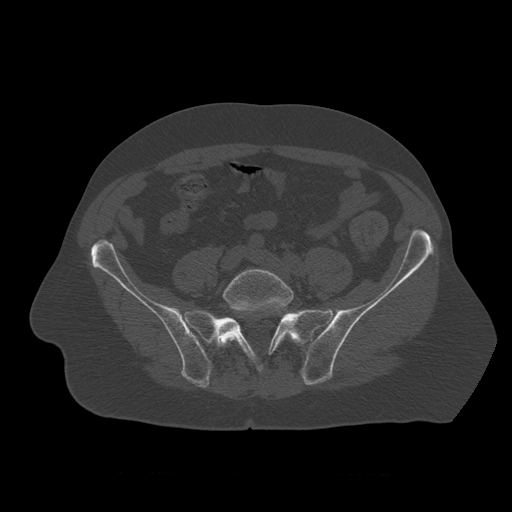
CT including the spine, one axial slice; position 244 of 450 along the scan axis; bone window (W 1800 / L 400 HU); 1.25 mm slice thickness; 512 × 512 image matrix. Patient age 75 years. Case-level facts recorded for this patient, not image findings: primary cancer: prostate.
Structures marked on this image (semi-automatic segmentation, software-assisted and operator-edited):
- L5 vertebra: bounding box [x1, y1, x2, y2] px = [223, 269, 295, 346]